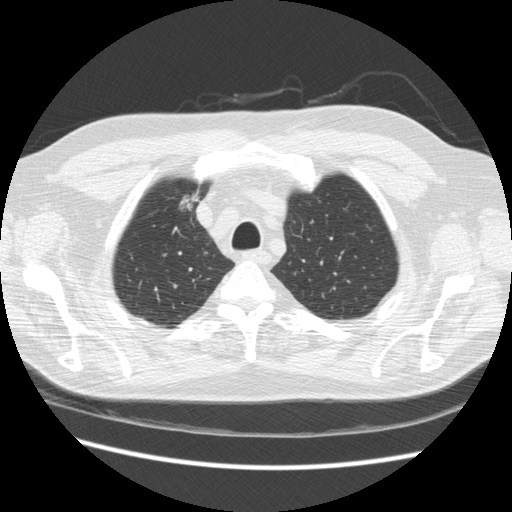
Axial slice from a low-dose chest CT screening exam, third screening round (two years after baseline), lung window (W 1500 / L -600 HU), 2.5 mm slice thickness, standard (soft-tissue) reconstruction kernel (STANDARD), 120 kVp. Male participant, aged 66 years at enrolment. Former smoker at enrolment.
Lesion marked by an expert reader, bounding box <166,183,209,221> (left, top, right, bottom; pixels). No non-calcified nodule or mass ≥4 mm was recorded by the screening reader at this exam. Official screen result: positive, other. Later outcome: lung cancer diagnosed 229 days after this screen — bronchiolo-alveolar adenocarcinoma, NOS, right upper lobe, moderately differentiated (G2), stage IA (AJCC 6th edition), 12 mm at pathology.